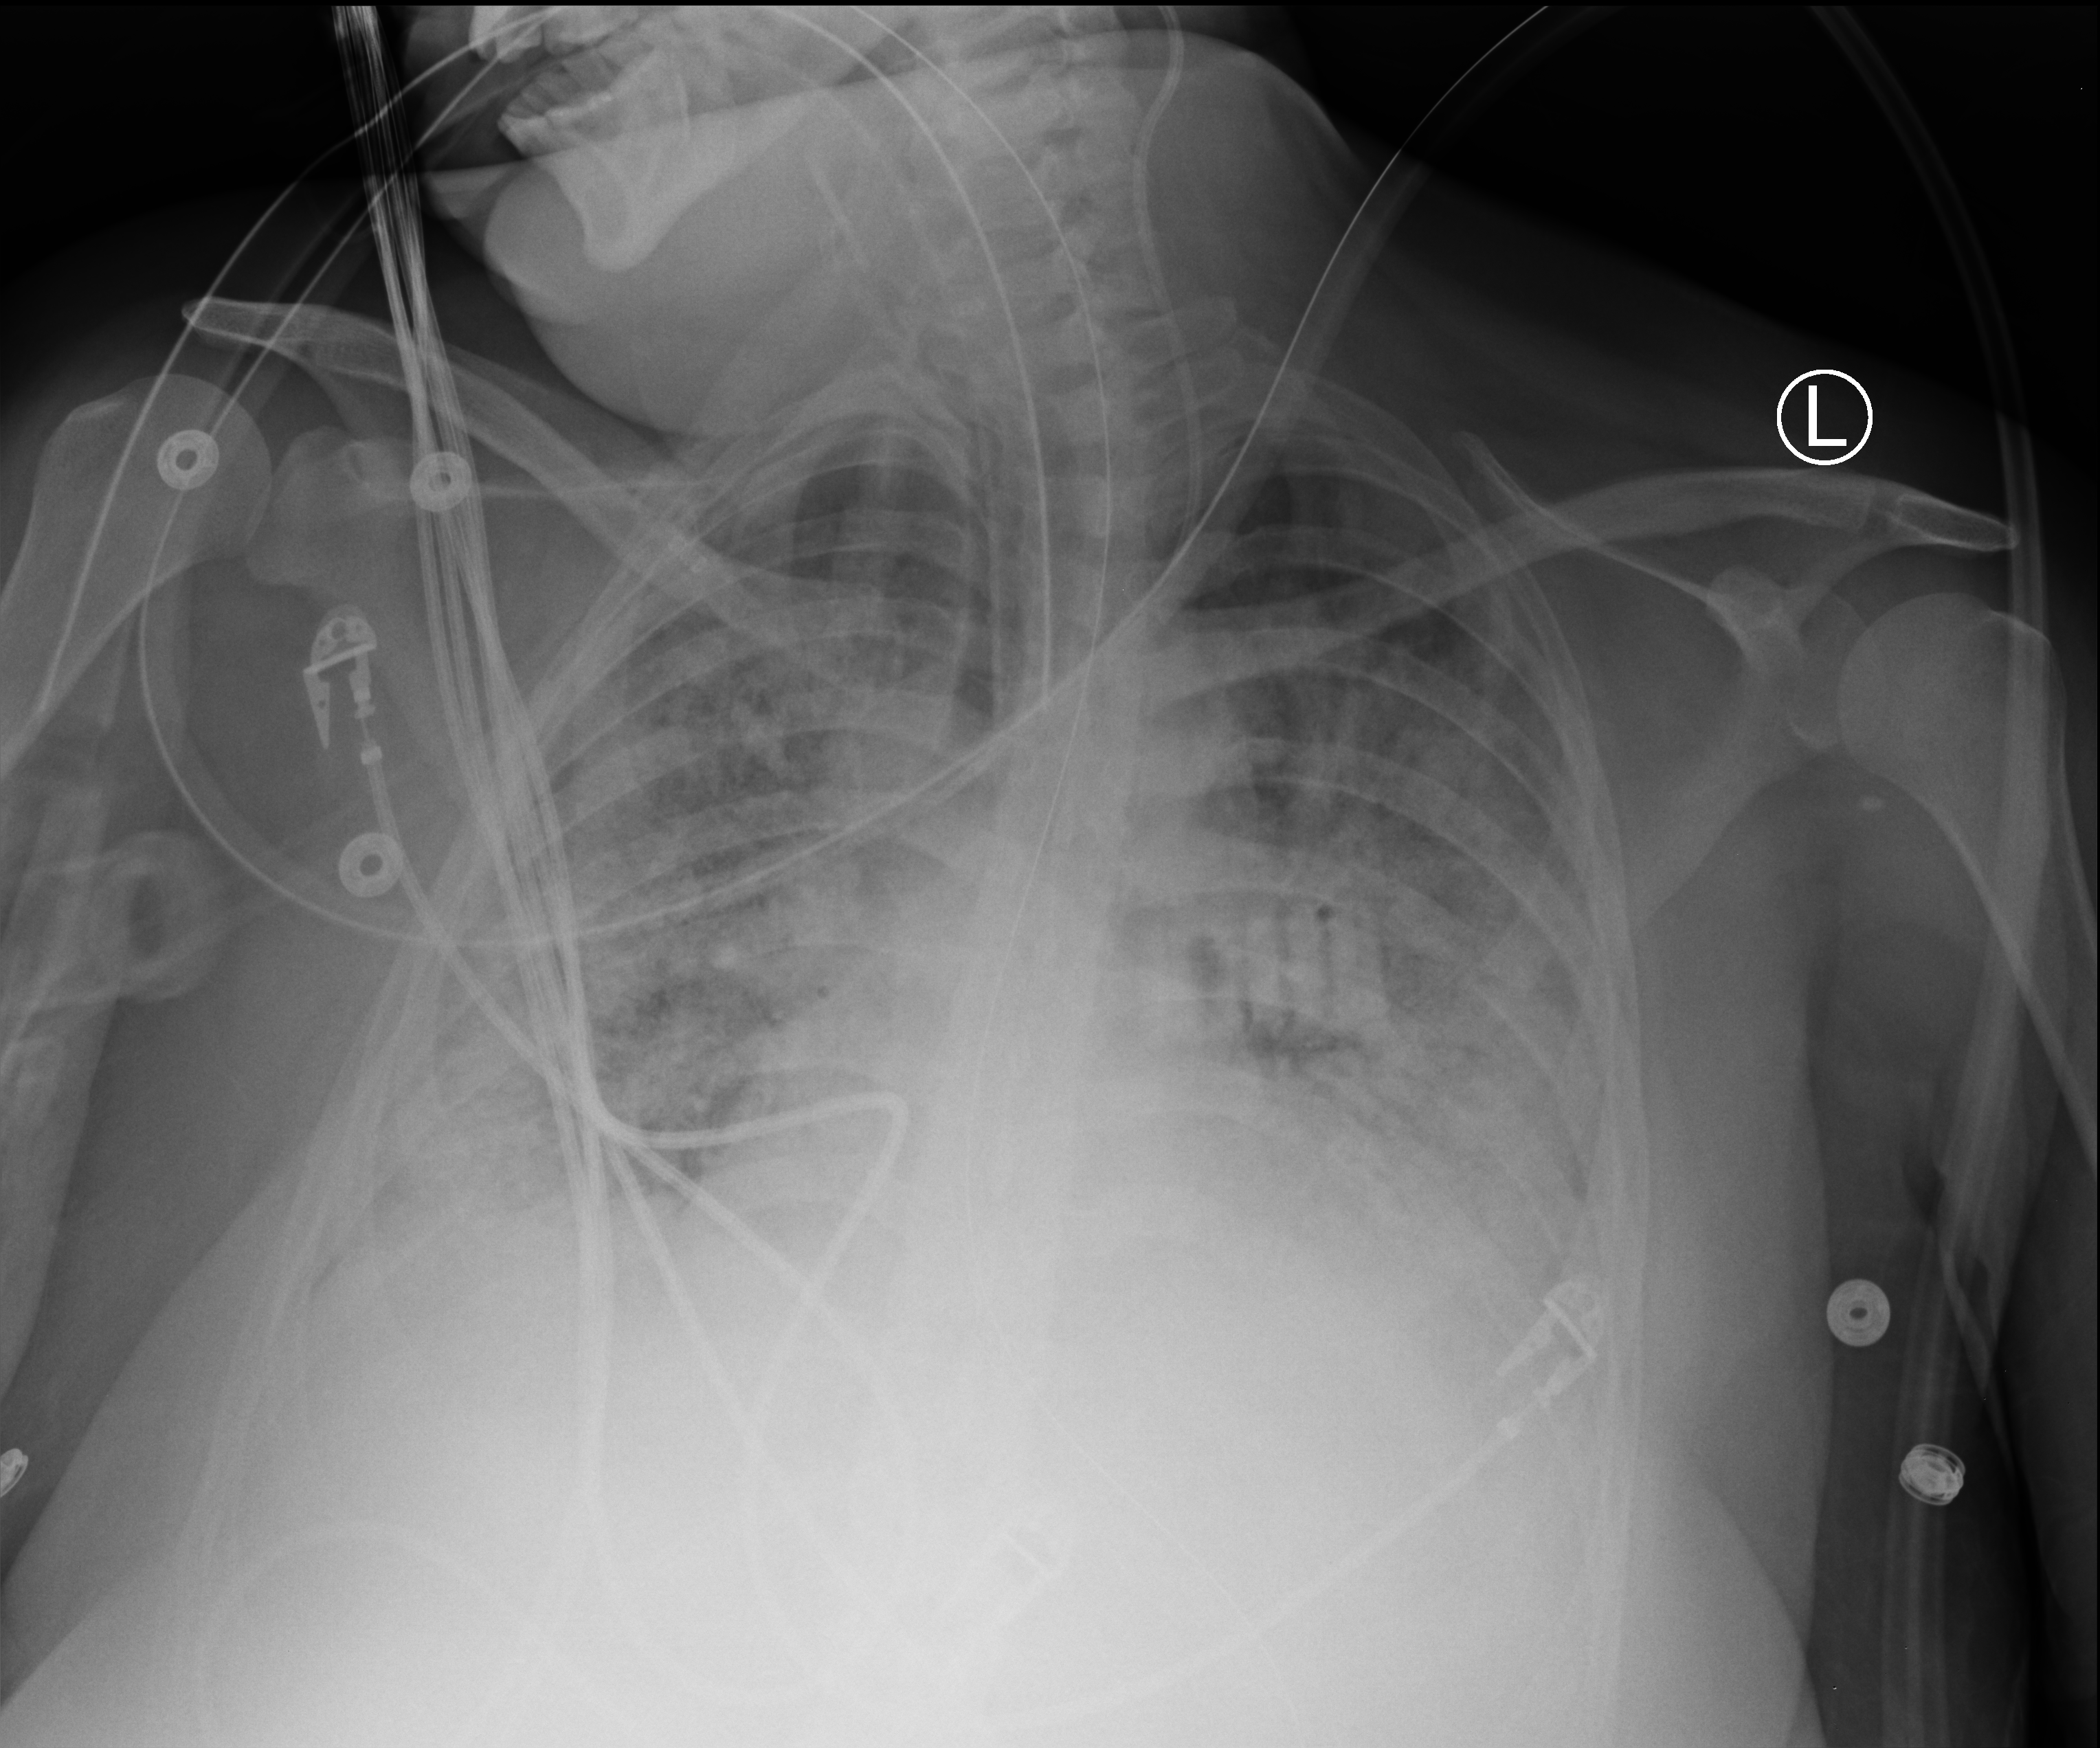
Chest X-ray (portable), anteroposterior (AP) projection. Patient hospitalised with COVID-19; female, aged 18–59 years.
Hospital-stay facts (about this admission, not read from this image; timing relative to this image not recorded):
- admitted to intensive care during this hospital stay: no
- mechanically ventilated during this hospital stay: yes